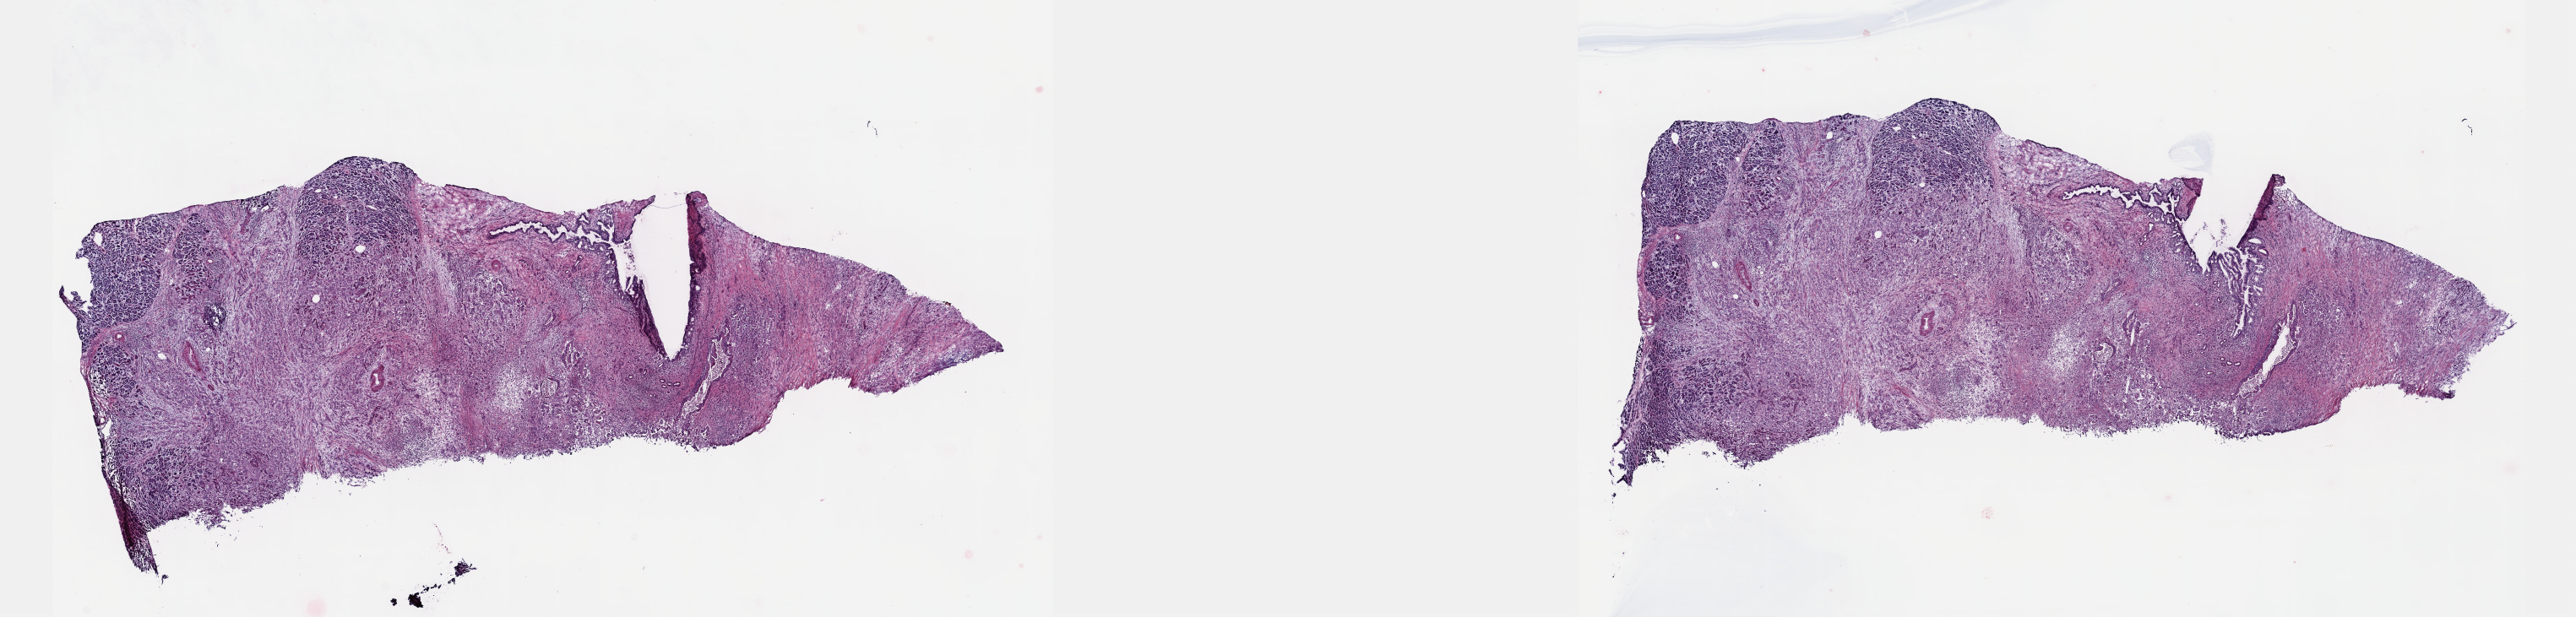
H&E-stained whole-slide image — shown as a low-resolution overview of the whole scanned area (about 24.6 x 5.9 mm, from a 40x scan), frozen section from the top of the tissue portion, pancreas, primary tumour sample. Female, age 63 years at initial diagnosis. Histologic grade: G3 (poorly differentiated). Slide review estimates, as recorded: tumour cells 70%, tumour nuclei 70%, normal cells 0%, stromal cells 30%, necrosis 0%. Infiltration values recorded for this section: lymphocyte infiltration 70%, monocyte infiltration 10%, neutrophil infiltration 10%.
AJCC pathologic stage: IIB. Lymph nodes positive (case pathology): 3 of 12 examined. Diagnosis: Infiltrating duct carcinoma, NOS. TNM: T3 N1 MX.